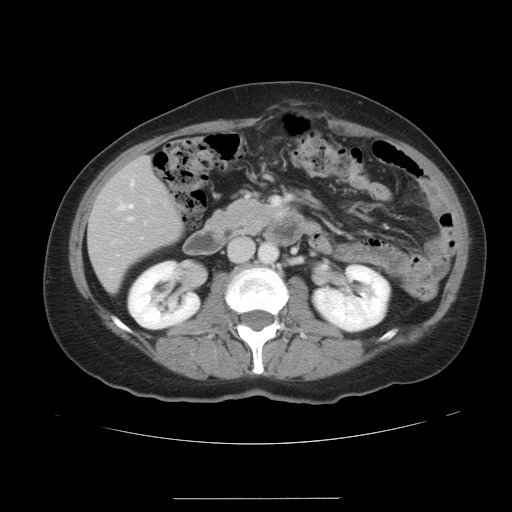
Contrast-enhanced abdominal CT, one axial slice; slice 14 of 41 in the series (ordered by position); 120 kVp; intravenous contrast given; soft-tissue window (W 400 / L 40 HU); 5 mm slice thickness; 512 × 512 image matrix, field of view 381 × 381 mm. Female patient, age 63 years. From the clinical record (not read from this slice): diagnosis: colorectal cancer liver metastases, imaged before liver resection; multiple liver metastases: yes.
Annotated regions visible in this slice (manually delineated by an expert):
- hepatic veins: bounding box (x1, y1, x2, y2) in pixels: (119, 205, 132, 210)
- liver: (90, 159, 183, 291)
- planned liver remnant (the part of the liver to remain after resection): (90, 176, 183, 291)
- portal vein (with intrahepatic branches): (127, 216, 134, 221)